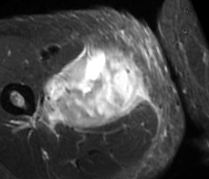
MRI of an extremity soft-tissue mass, one axial slice; slice 35 of 89 in the series (ordered by position); STIR; MR volume resampled by the dataset authors to the PET/CT grid (not the native acquisition matrix); 3.27 mm slice thickness; 209 × 179 image matrix, field of view 204 × 175 mm. Male patient. From the clinical record (not read from this slice): histological type: undifferentiated - pleiomorphic; grade: high; site of the primary tumour: right thigh.
Outlined on this slice (expert contour drawn on MRI and transferred to this co-registered scan by the dataset authors):
- gross tumour volume including surrounding oedema: bounding box (x1, y1, x2, y2) in pixels: (34, 44, 147, 127)
- gross tumour volume (mass): (59, 48, 145, 127)